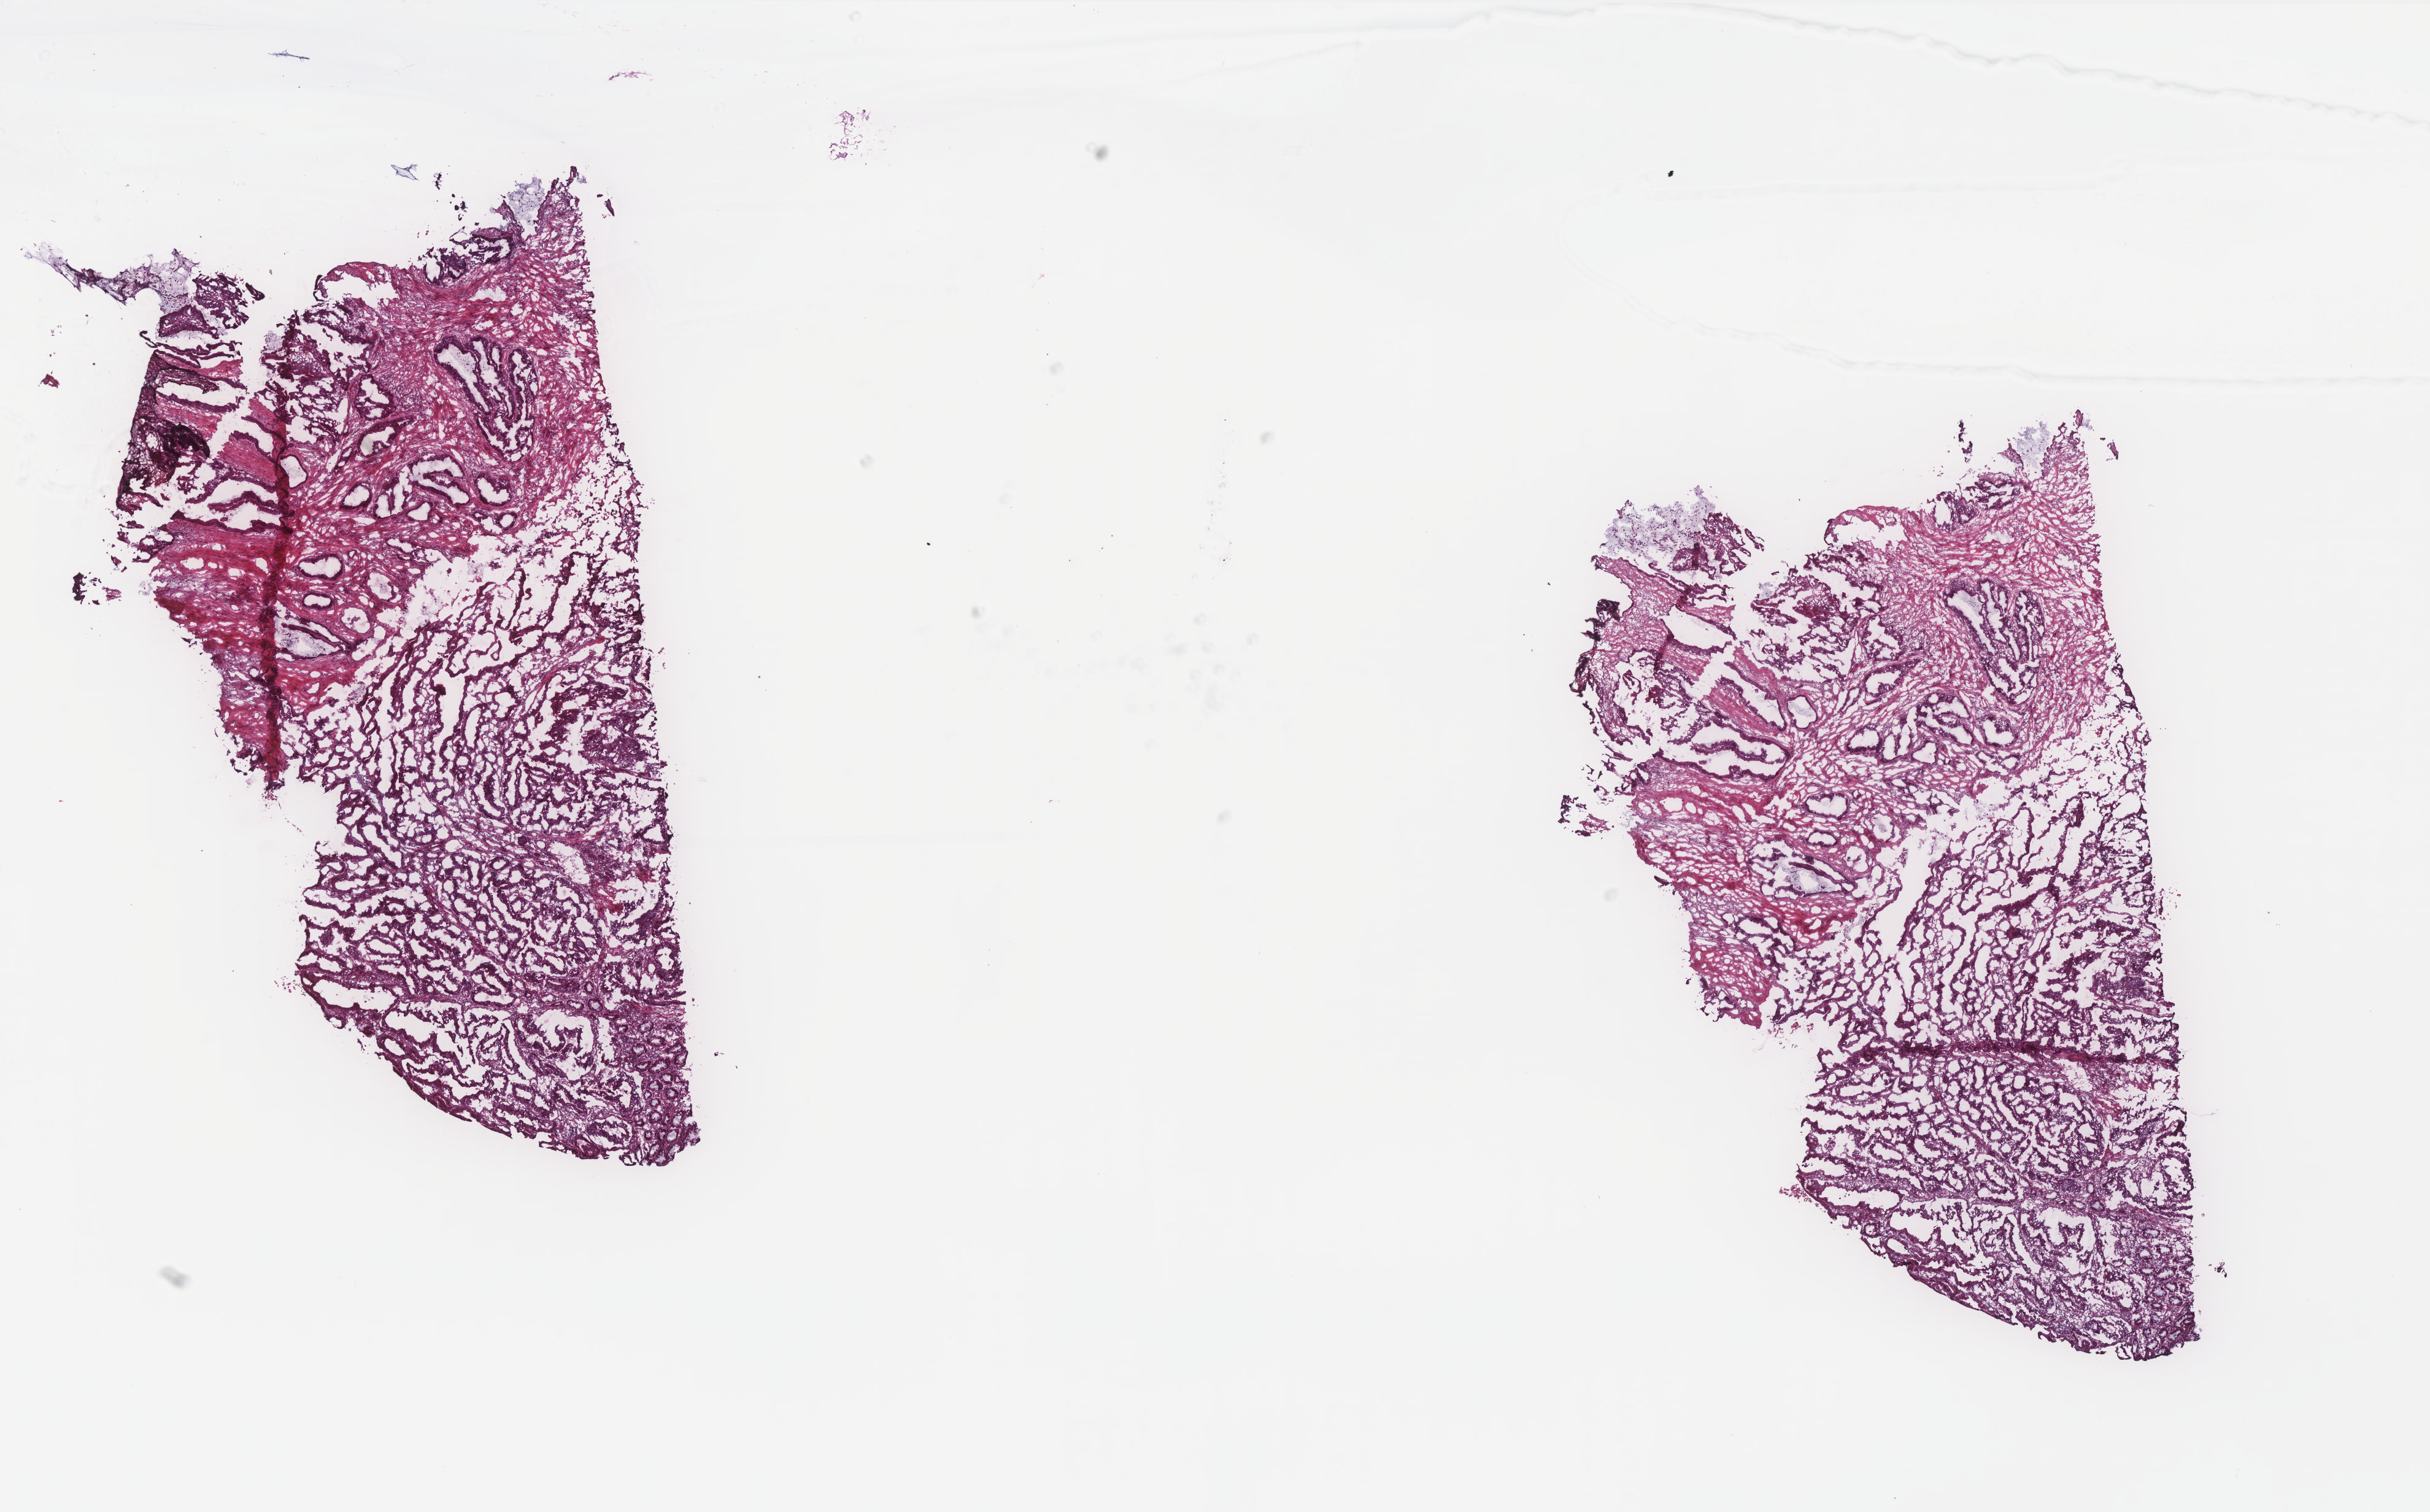
Digitized H&E tissue section (whole slide), low-resolution overview of the scanned area, about 15.9 x 9.9 mm (from a 40x scan). Frozen section. Primary tumour sample from the colon. Male patient; age at initial diagnosis 82 years. Composition of this section per pathologist review: tumour cells 100%, tumour nuclei 80%, normal cells 0%, stromal cells 0%, necrosis 0%. Inflammatory infiltration, as recorded: lymphocyte infiltration 0%, monocyte infiltration 0%, neutrophil infiltration 0%.
Diagnosis: Mucinous adenocarcinoma (sigmoid colon). AJCC pathologic stage: IIA. Lymph nodes positive (case pathology): 0 of 15 examined.